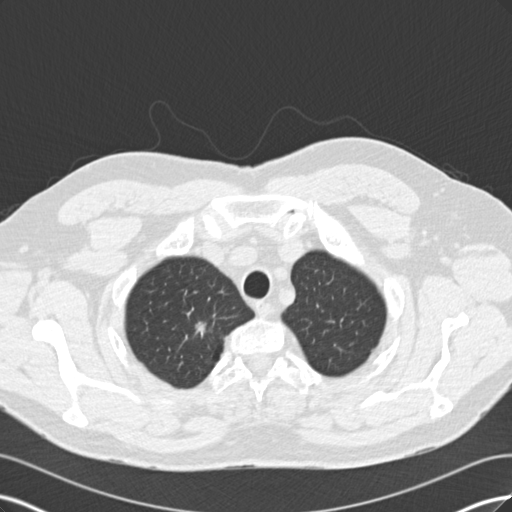
Low-dose screening chest CT, one axial slice. Slice 151 of 171 in the series (ordered by position). Reconstruction kernel B30f. Lung window (W 1500 / L -600 HU). 2 mm slice thickness. 512 × 512 image matrix, field of view 360 × 360 mm.
Outlined on this slice (manually delineated by an expert):
- lesion 1 (tumor, upper lobe of right lung): box from (x=195, y=322) to (x=206, y=337) px